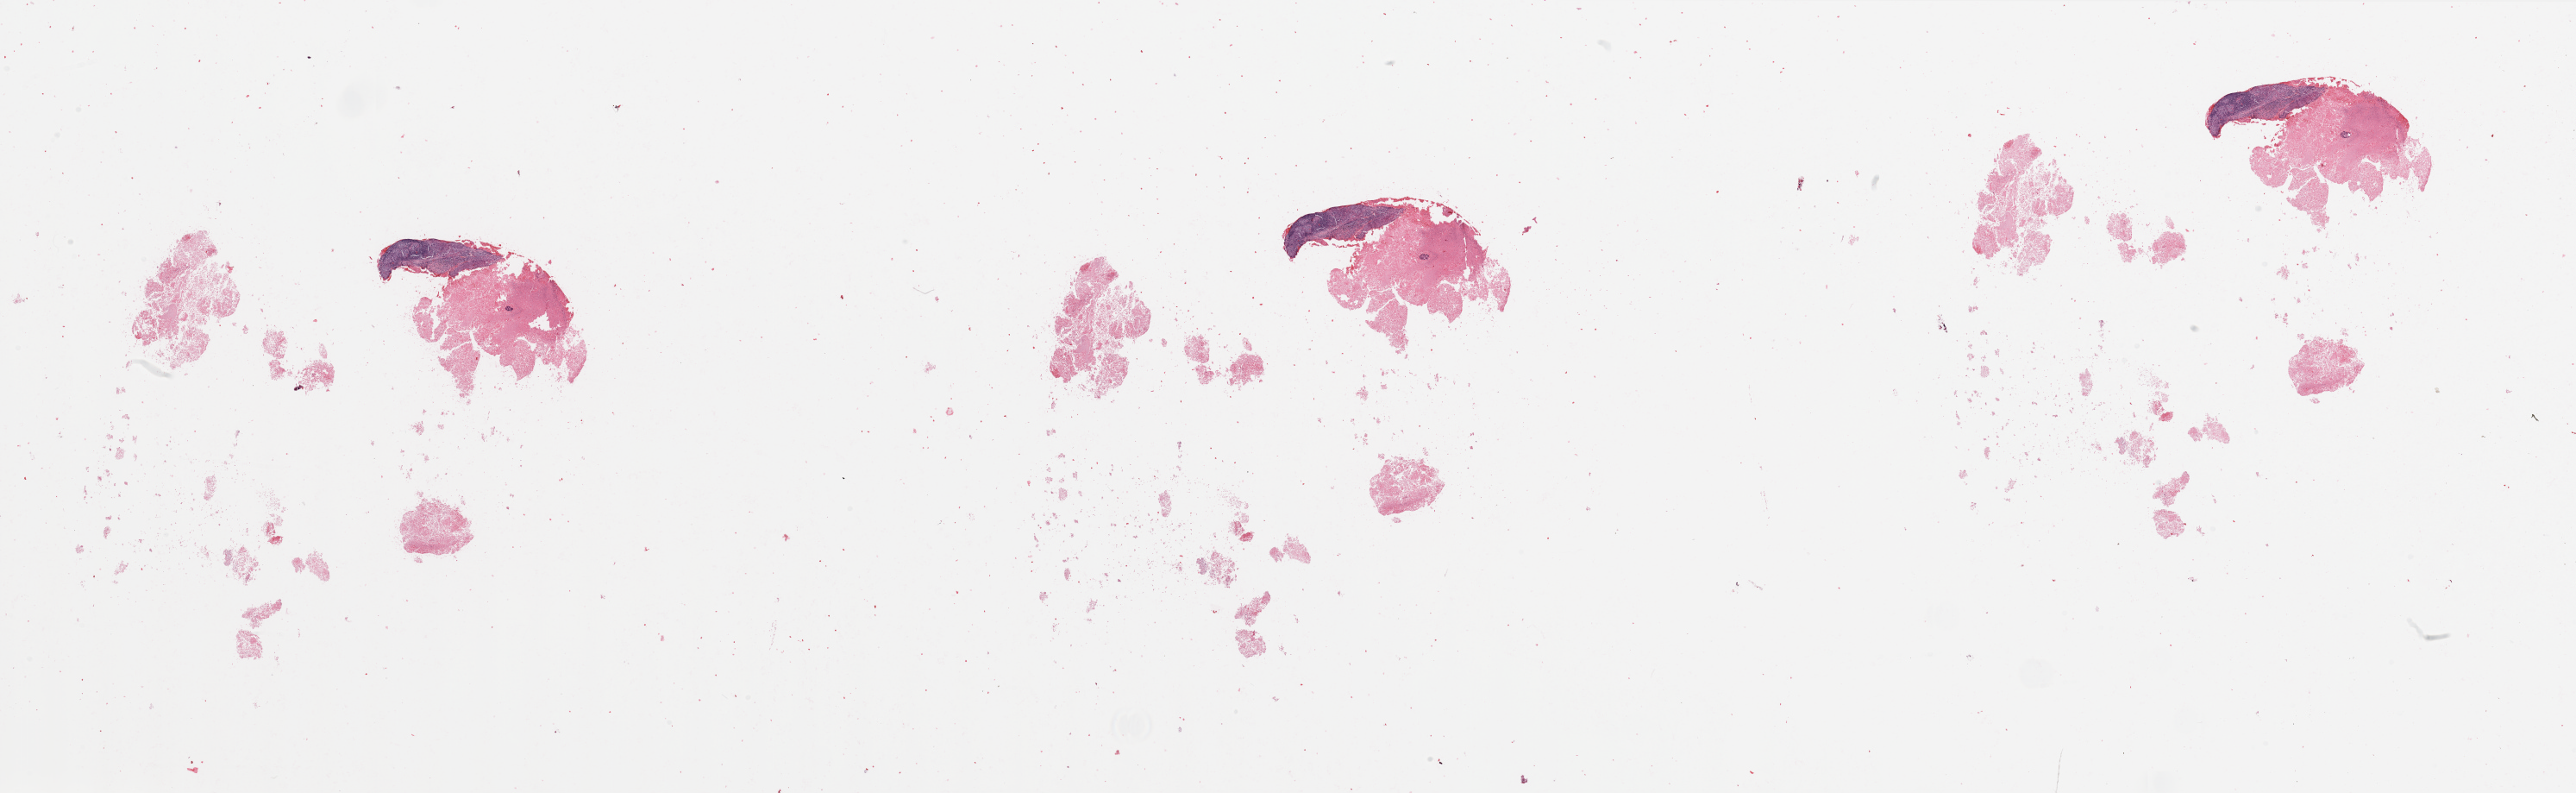
Digitized H&E-stained tissue section (whole slide) — shown as a low-resolution overview of the whole scanned area (about 47.3 x 14.5 mm). Lung, tumour tissue. 74-year-old male patient. Histologic grade: G2 (moderately differentiated).
AJCC pathologic stage: IB. Primary tumour site (as recorded): right upper lobe. Histologic diagnosis: Squamous cell carcinoma, NOS.